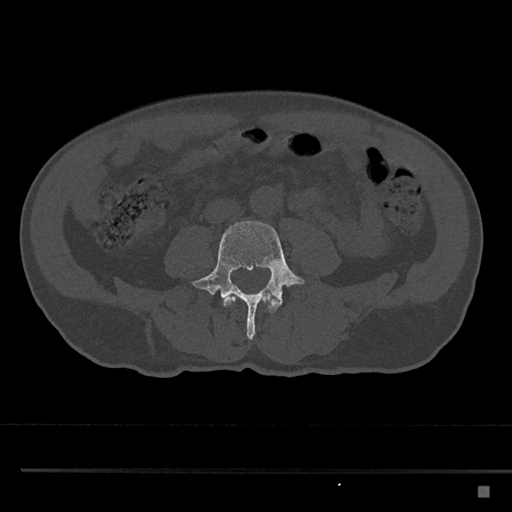
CT including the spine, one axial slice; position 642 of 797 along the scan axis; reconstruction kernel Br40s/3; bone window (W 1800 / L 400 HU); 512 × 512 image matrix, field of view 391 × 391 mm. Male patient, age 59 years. From the clinical record (not read from this slice): primary cancer: prostate.
Annotated regions visible in this slice (semi-automatic segmentation, software-assisted and operator-edited):
- L3 vertebra: bounding box (x1, y1, x2, y2) in pixels: (223, 296, 278, 313)
- L4 vertebra: (192, 221, 305, 340)